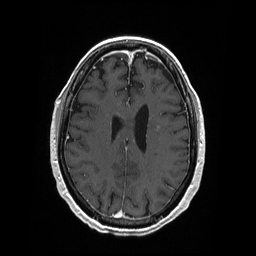
Brain MRI from a brain-tumour surgery series, one axial slice. Position 78 of 208 along the scan axis. T1-weighted post-contrast. 1 mm slice thickness. 256 × 256 image matrix, field of view 256 × 256 mm. Case-level facts recorded for this patient, not image findings: histopathology: Primary diffuse large B-cell lymphoma.
Outlined on this slice (outlined manually by an expert reader):
- tumour: bounding box <157,126,160,130> (left, top, right, bottom; pixels)